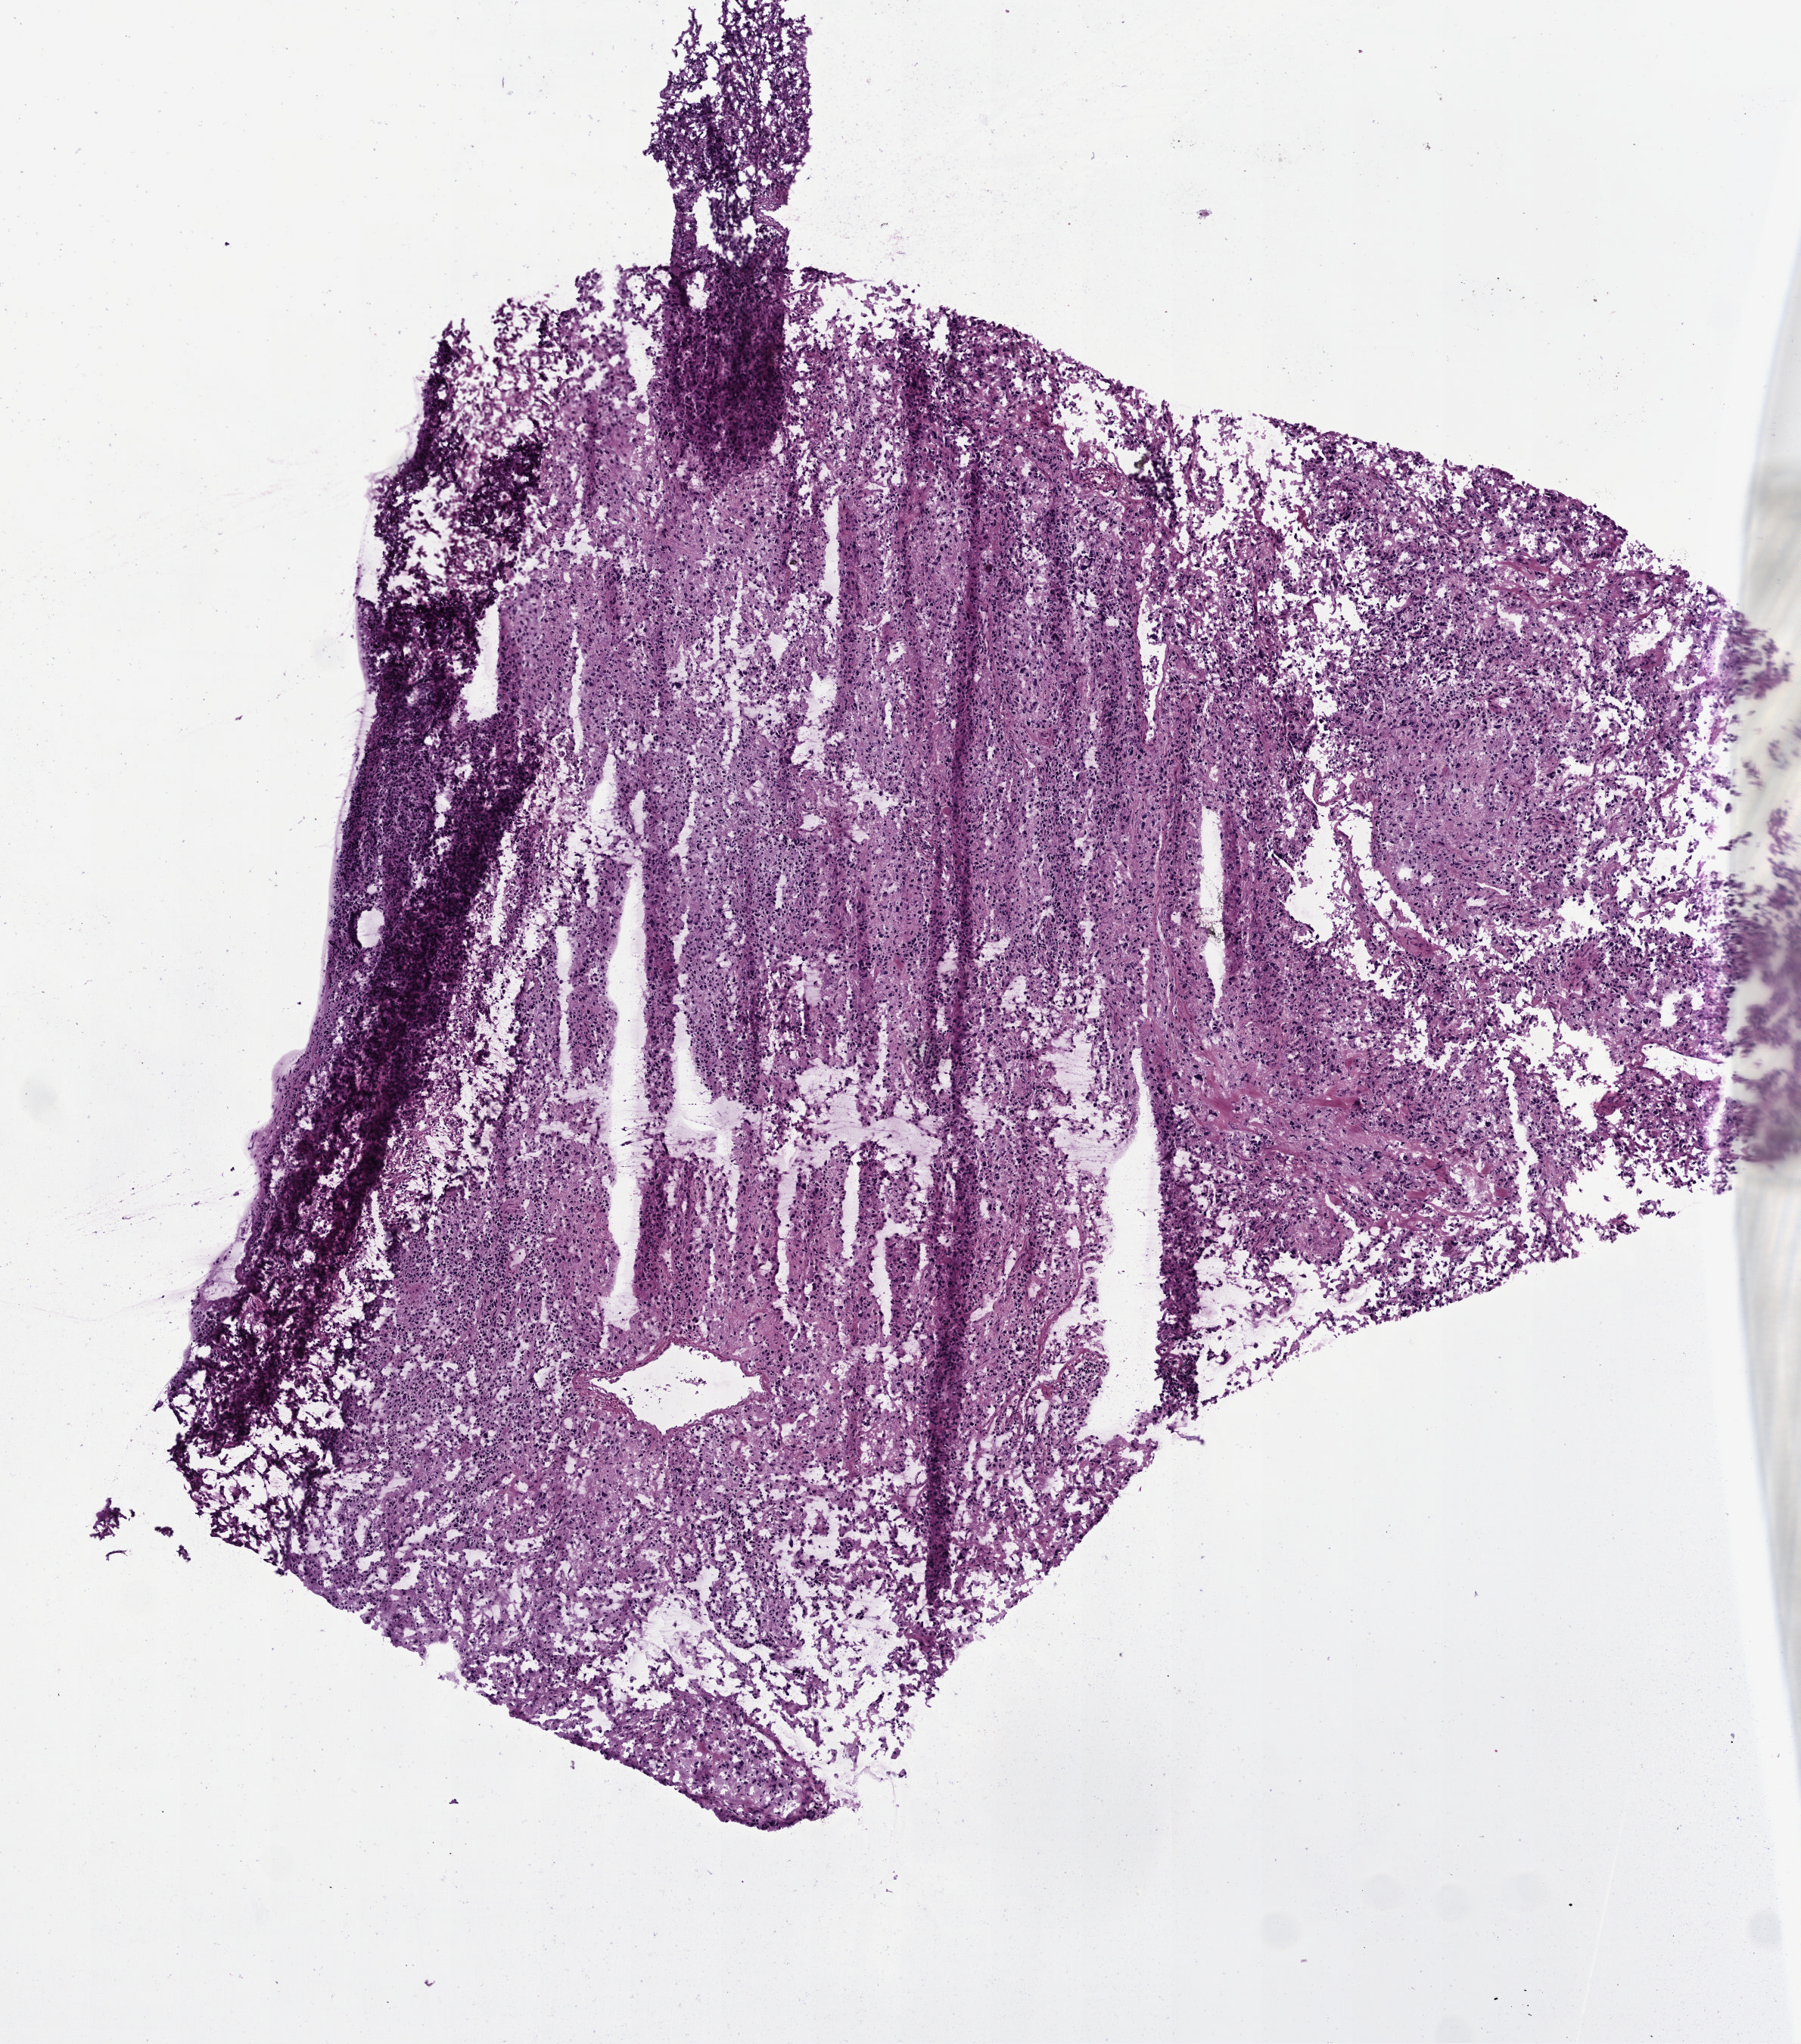
Whole-slide histology image, H&E-stained — a low-resolution overview of the entire scanned area, about 4.7 x 5.3 mm; frozen section from the top of the tissue portion; primary tumour sample from the adrenal gland. Female patient; age at initial diagnosis 49 years. Slide review estimates, as recorded: tumour cells 90%, tumour nuclei 90%, normal cells 0%, stromal cells 10%, necrosis 0%. Inflammatory infiltration, as recorded: lymphocyte infiltration 40%, monocyte infiltration 20%, neutrophil infiltration 20%.
- histologic diagnosis: Pheochromocytoma, malignant
- laterality: right